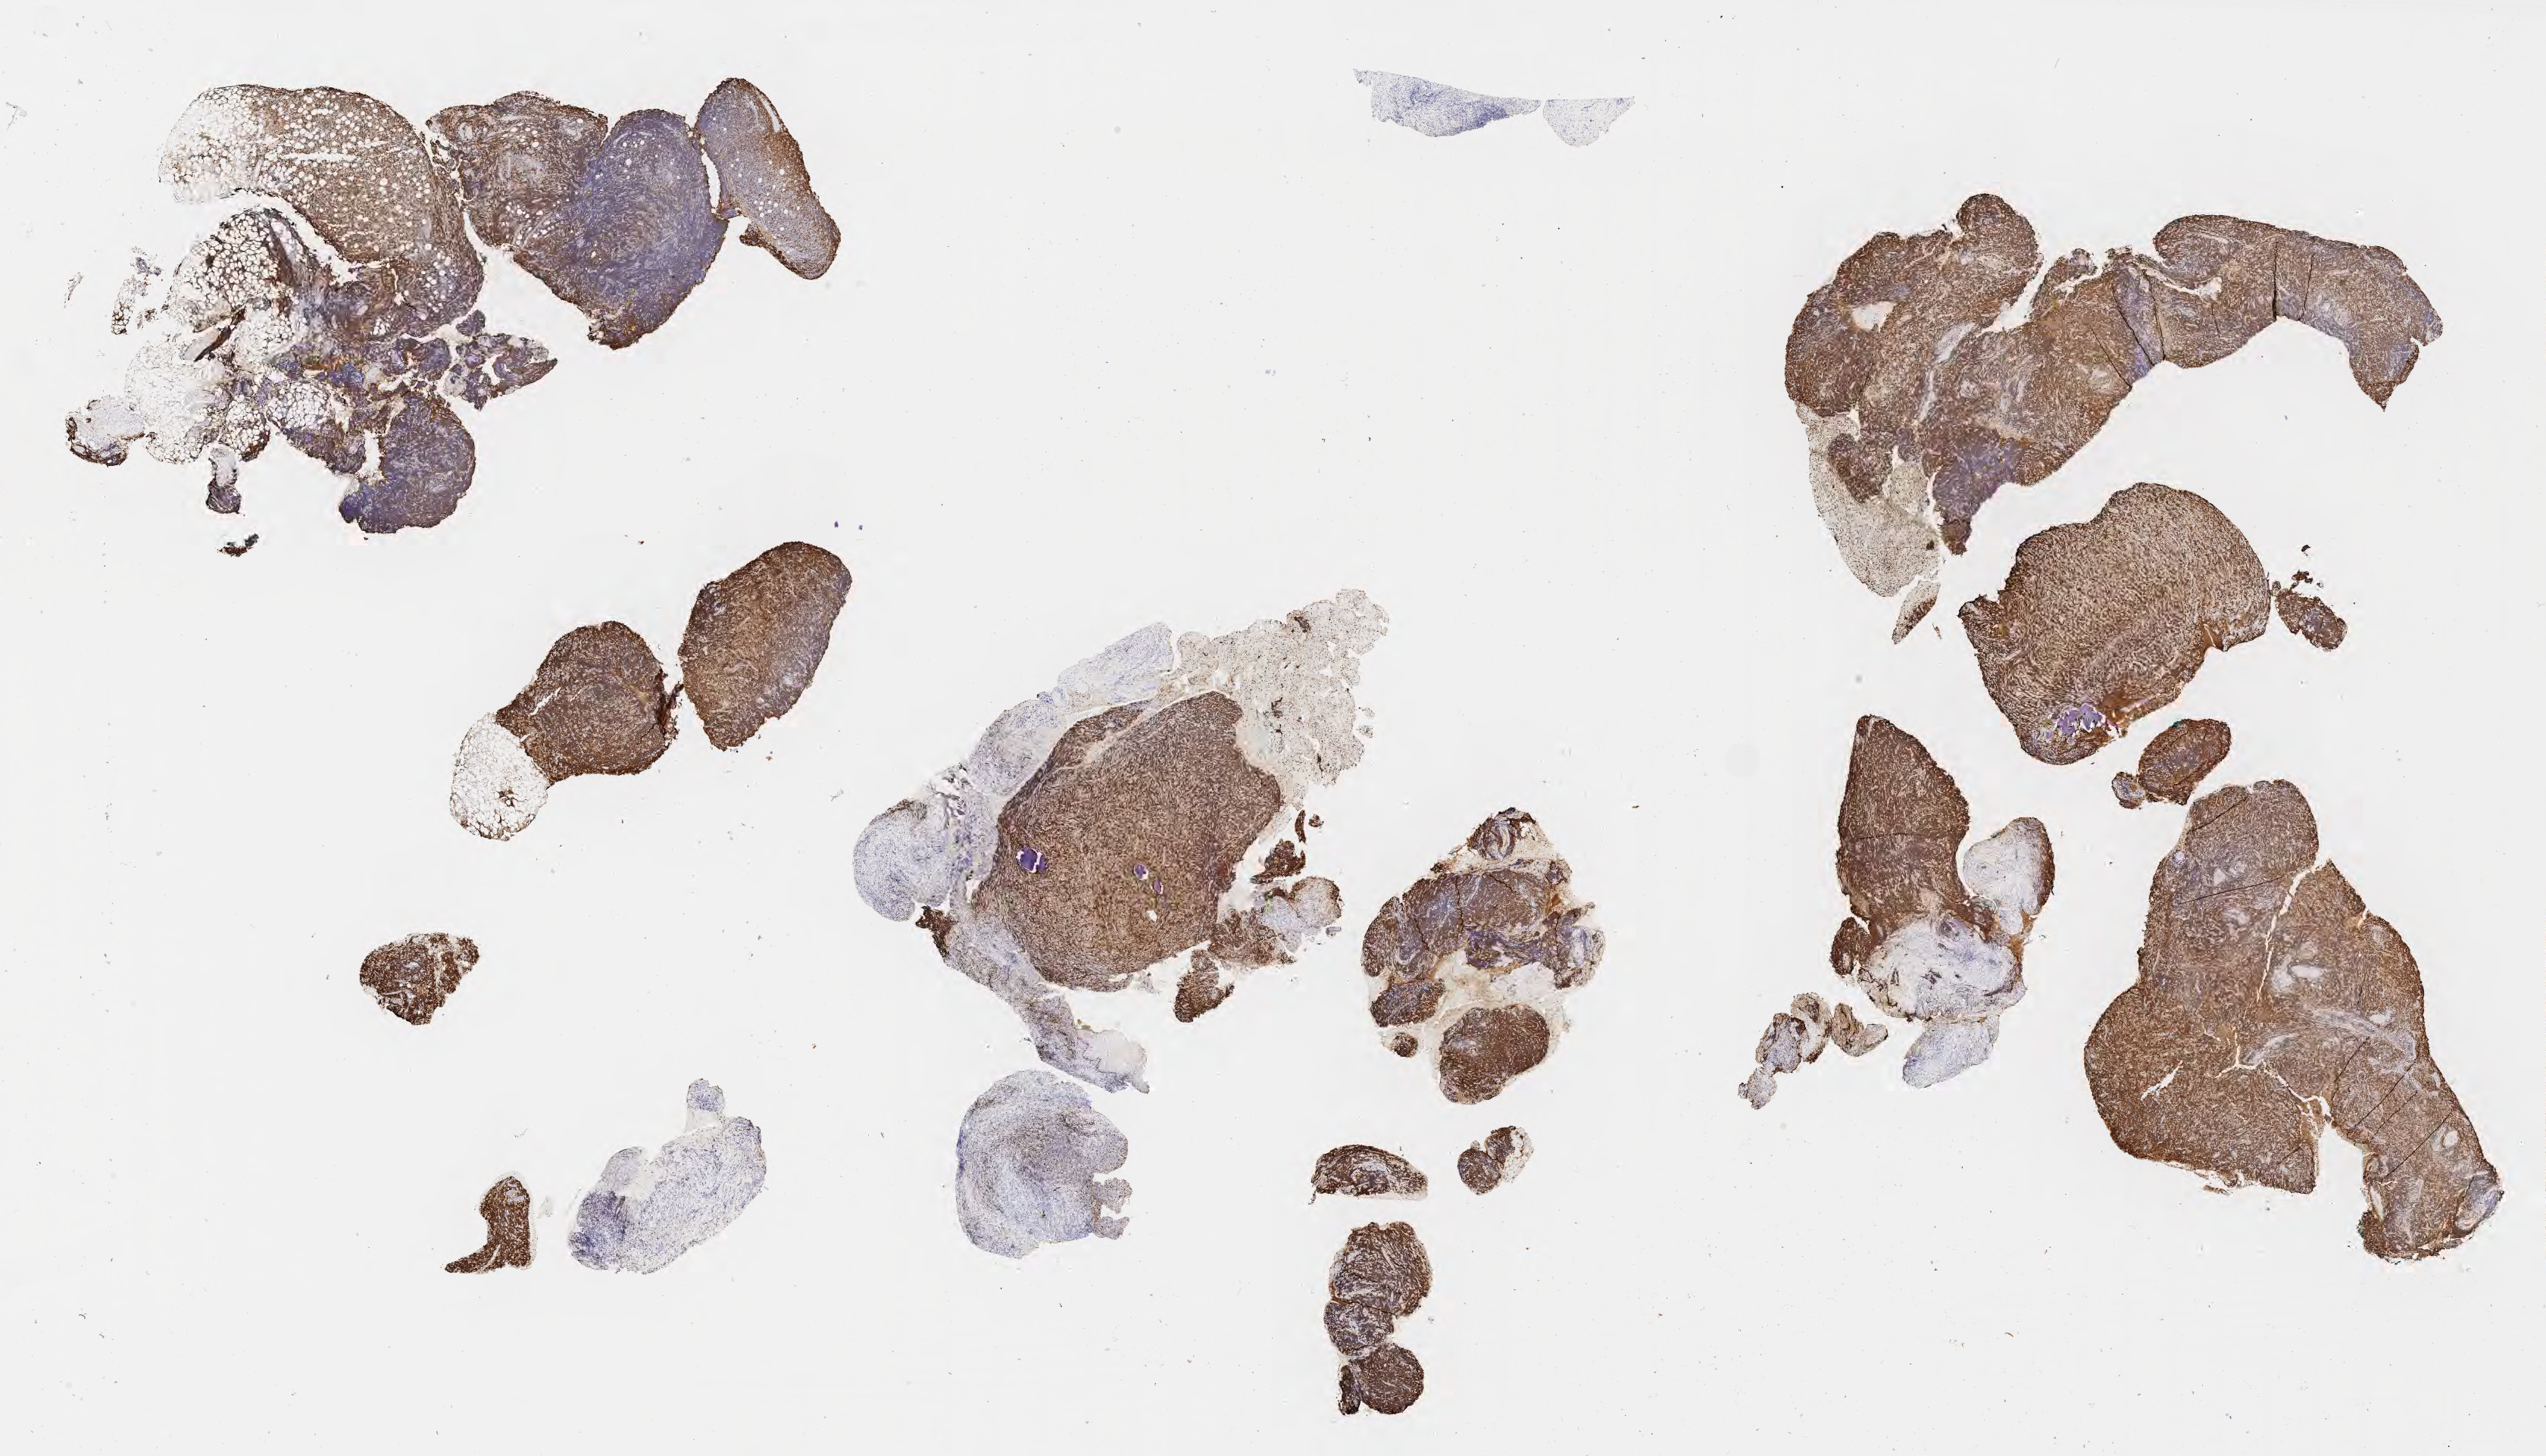
IHC for Ki-67, whole-slide image — whole scanned area (about 27.2 x 15.5 mm) shown as a low-resolution overview. Specimen: tumor tissue. Patient: male, age 45 years.
- diagnosis: Diffuse large B-cell lymphoma, NOS